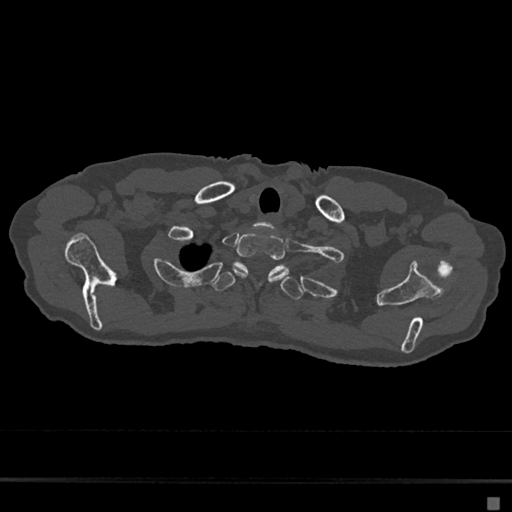
CT including the spine, one axial slice. Position 596 of 797 along the scan axis. Reconstruction kernel Br40s/3. 120 kVp. Bone window (W 1800 / L 400 HU). 512 × 512 image matrix, field of view 360 × 360 mm. Patient: female, 68 years. Case-level facts recorded for this patient, not image findings: primary cancer: renal.
Outlined on this slice (semi-automatic segmentation, software-assisted and operator-edited):
- T1 vertebra: bounding box [x1, y1, x2, y2] px = [232, 232, 290, 282]
- T2 vertebra: [212, 262, 304, 300]